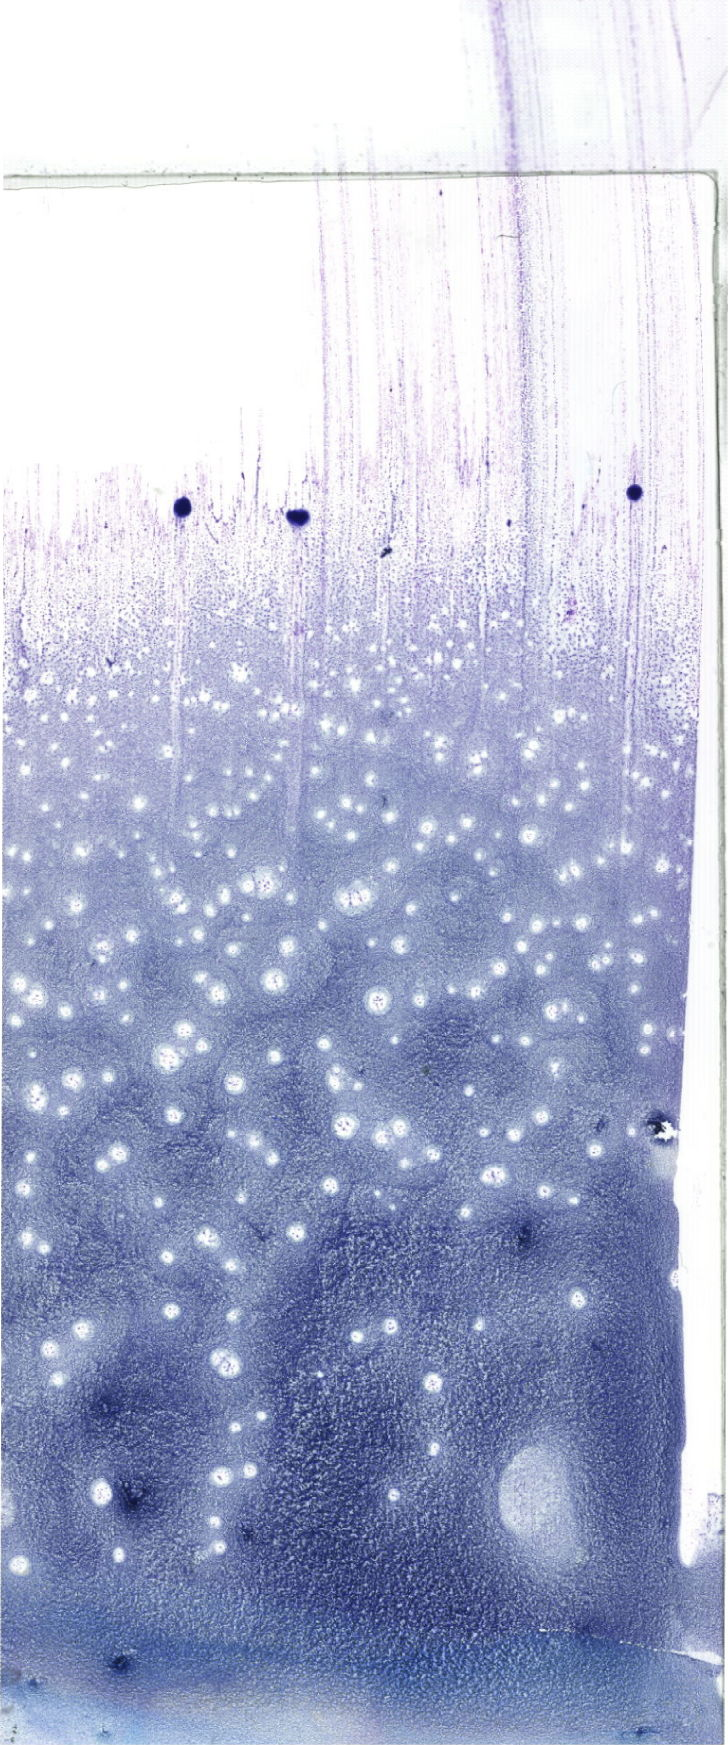
Bone marrow aspirate smear, May-Grünwald-Giemsa (MGG) stain, whole-slide image — low-resolution overview of the scanned area, about 20.6 x 49.5 mm. Female patient.
Diagnosis: B Acute Lymphoblastic Leukemia.